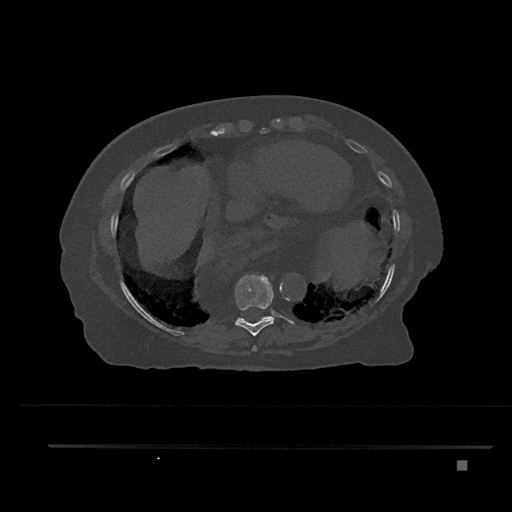
CT including the spine, one axial slice; slice 392 of 797 in the series (ordered by position); reconstruction kernel Br40s/3; 120 kVp; bone window (W 1800 / L 400 HU); 512 × 512 image matrix. Female patient, age 76 years. Case-level facts recorded for this patient, not image findings: primary cancer: lung.
Annotated regions visible in this slice (semi-automatic segmentation, software-assisted and operator-edited):
- T10 vertebra: box from (x=238, y=316) to (x=271, y=320) px
- T8 vertebra: (x=252, y=345)–(x=257, y=351)
- T9 vertebra: (x=235, y=275)–(x=274, y=336)